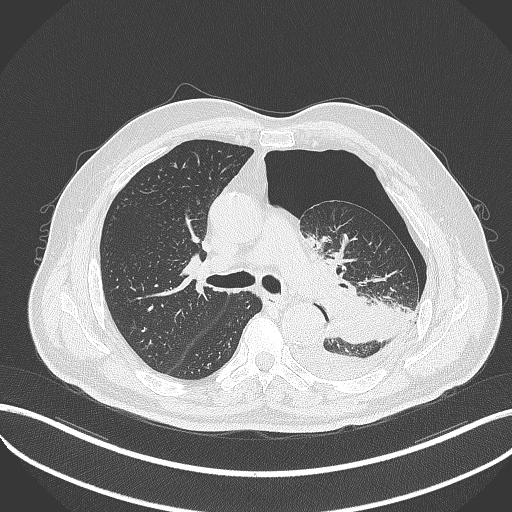
Chest CT, one axial slice; slice 325 of 464 in the series (ordered by position); reconstruction kernel B70f; lung window (W 1500 / L -600 HU); 1 mm slice thickness; 512 × 512 image matrix, field of view 400 × 400 mm. Patient: male, 76 years. Case-level facts recorded for this patient, not image findings: clinical TNM (as recorded): T3 N0 M1b.
Outlined on this slice (bounding box drawn by a radiologist):
- lung tumour (recorded histology: adenocarcinoma): box from (x=324, y=283) to (x=405, y=343) px